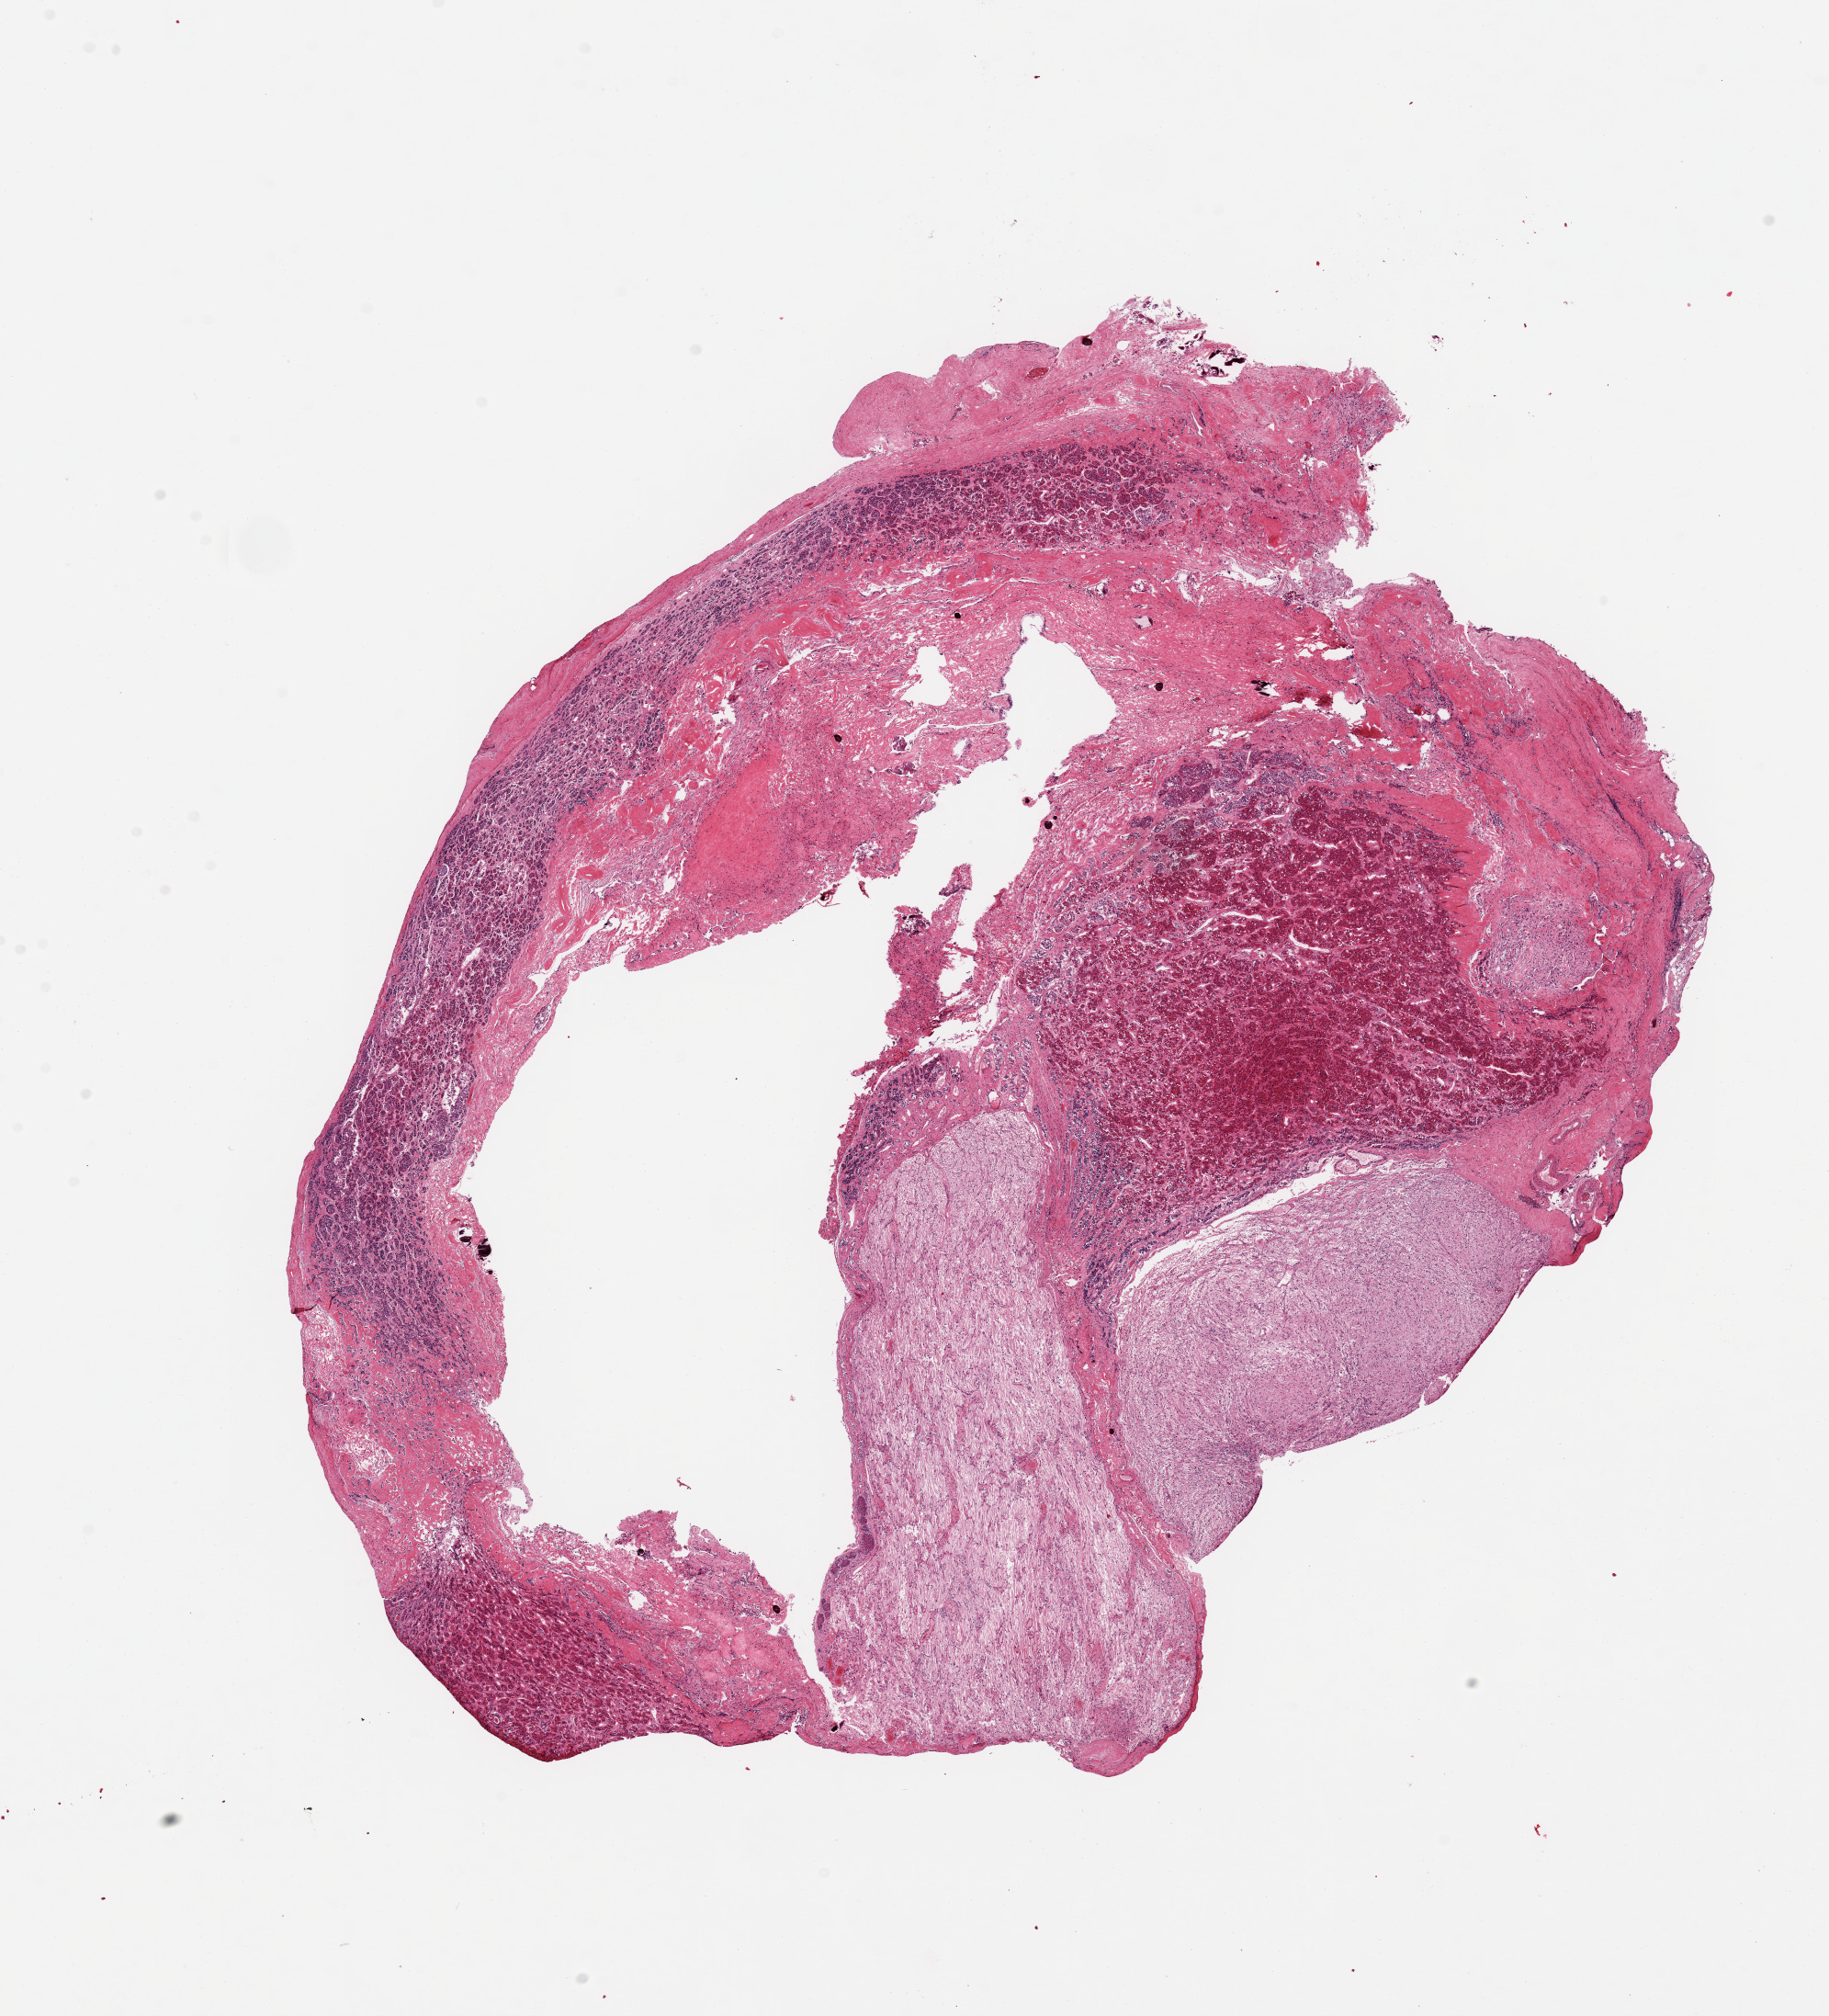
Digitized H&E-stained section — low-resolution overview of the scanned area, about 15.8 x 17.4 mm (from a 20x scan). PAXgene-fixed, paraffin-embedded tissue. Target tissue: pituitary. Tissue donor sample. Male donor.
Review note (as recorded): 1 piece; 60% neuro, 40% adenohypophysis.